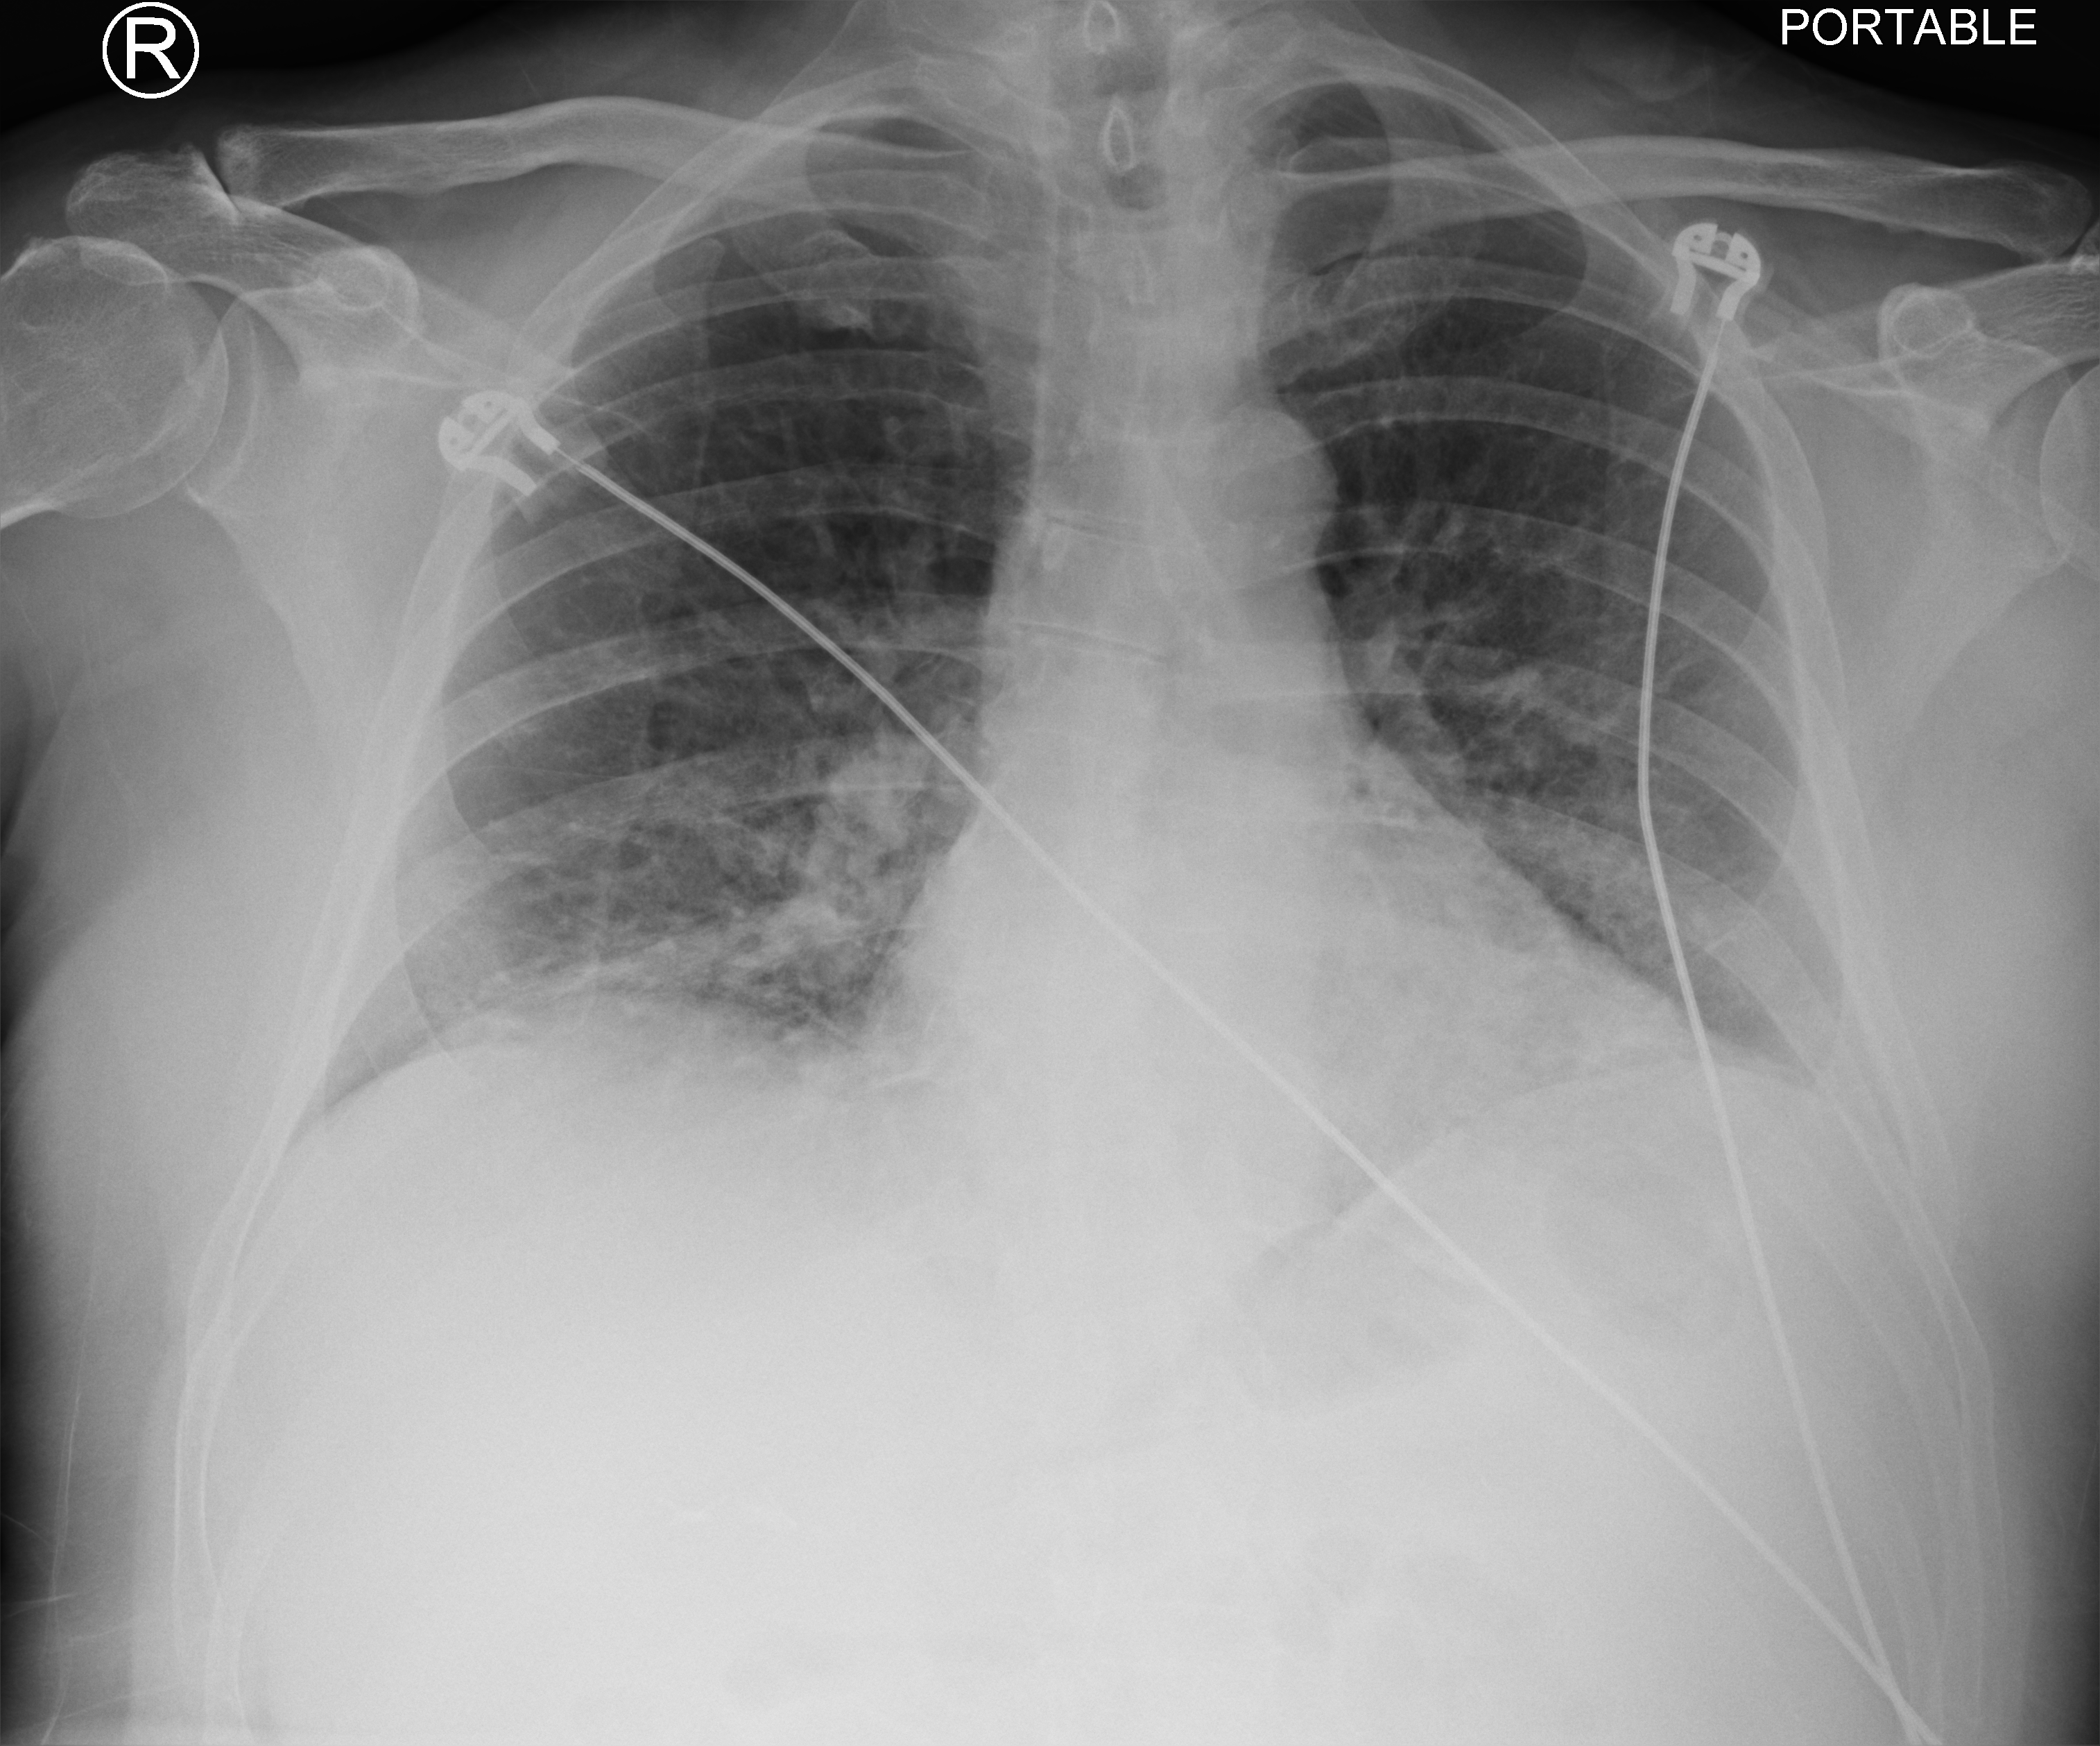
Bedside chest radiograph (computed radiography), anteroposterior (AP) projection. Male patient hospitalised with COVID-19, age 60–74 years.
Admission-level facts for this patient (not findings on this image; timing relative to this image not recorded): admitted to intensive care during this hospital stay: no.